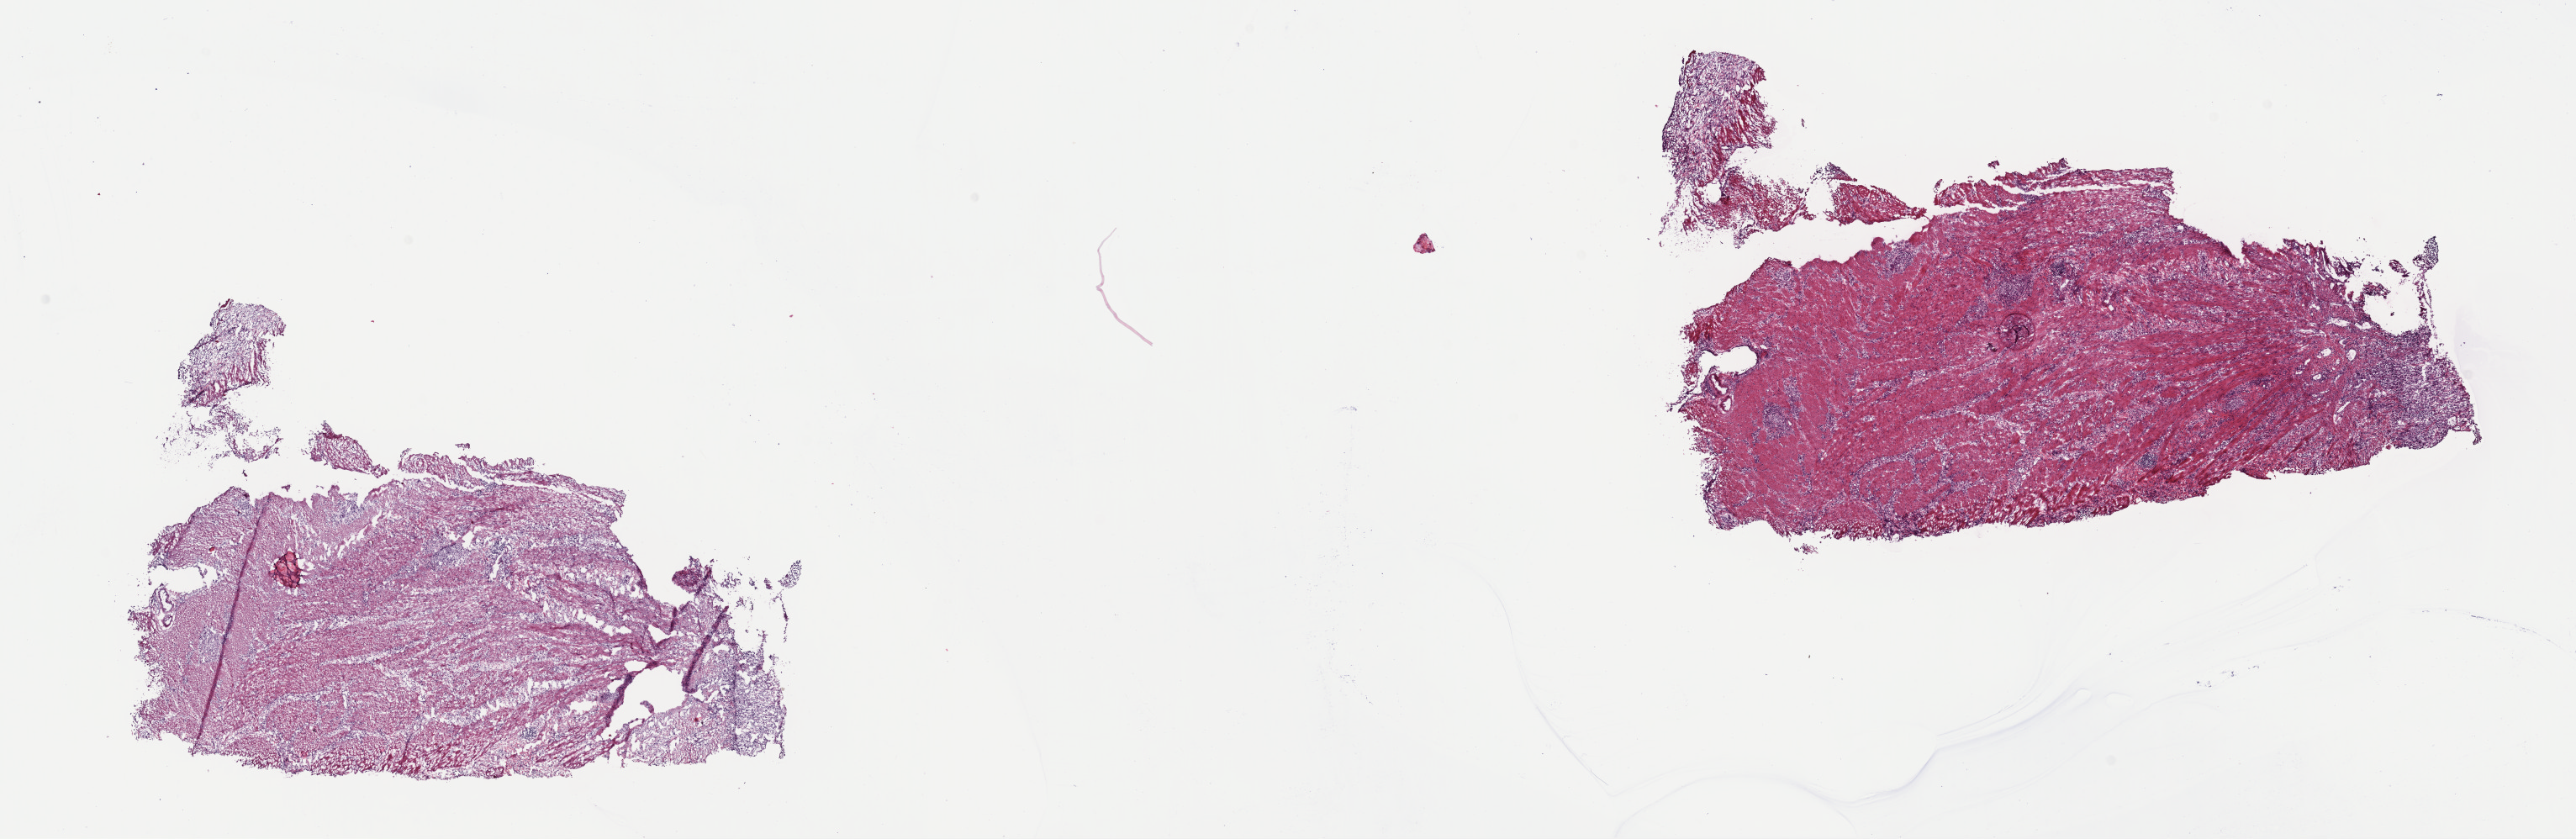
Digitized Hematoxylin and eosin (H&E) stained tissue section (whole slide), a low-resolution overview of the entire scanned area, about 24.2 x 7.9 mm, frozen section from the top of the tissue portion, primary tumour sample from the stomach. Male, age 47 years at initial diagnosis. Histologic grade: G3 (poorly differentiated). Composition of this section per pathologist review: tumour cells 100%, tumour nuclei 65%, normal cells 0%, stromal cells 0%, necrosis 0%. Inflammatory infiltration, as recorded: lymphocyte infiltration 0%, monocyte infiltration 0%, neutrophil infiltration 0%.
Diagnosis: Carcinoma, diffuse type (gastric antrum). AJCC pathologic stage: IIIB.